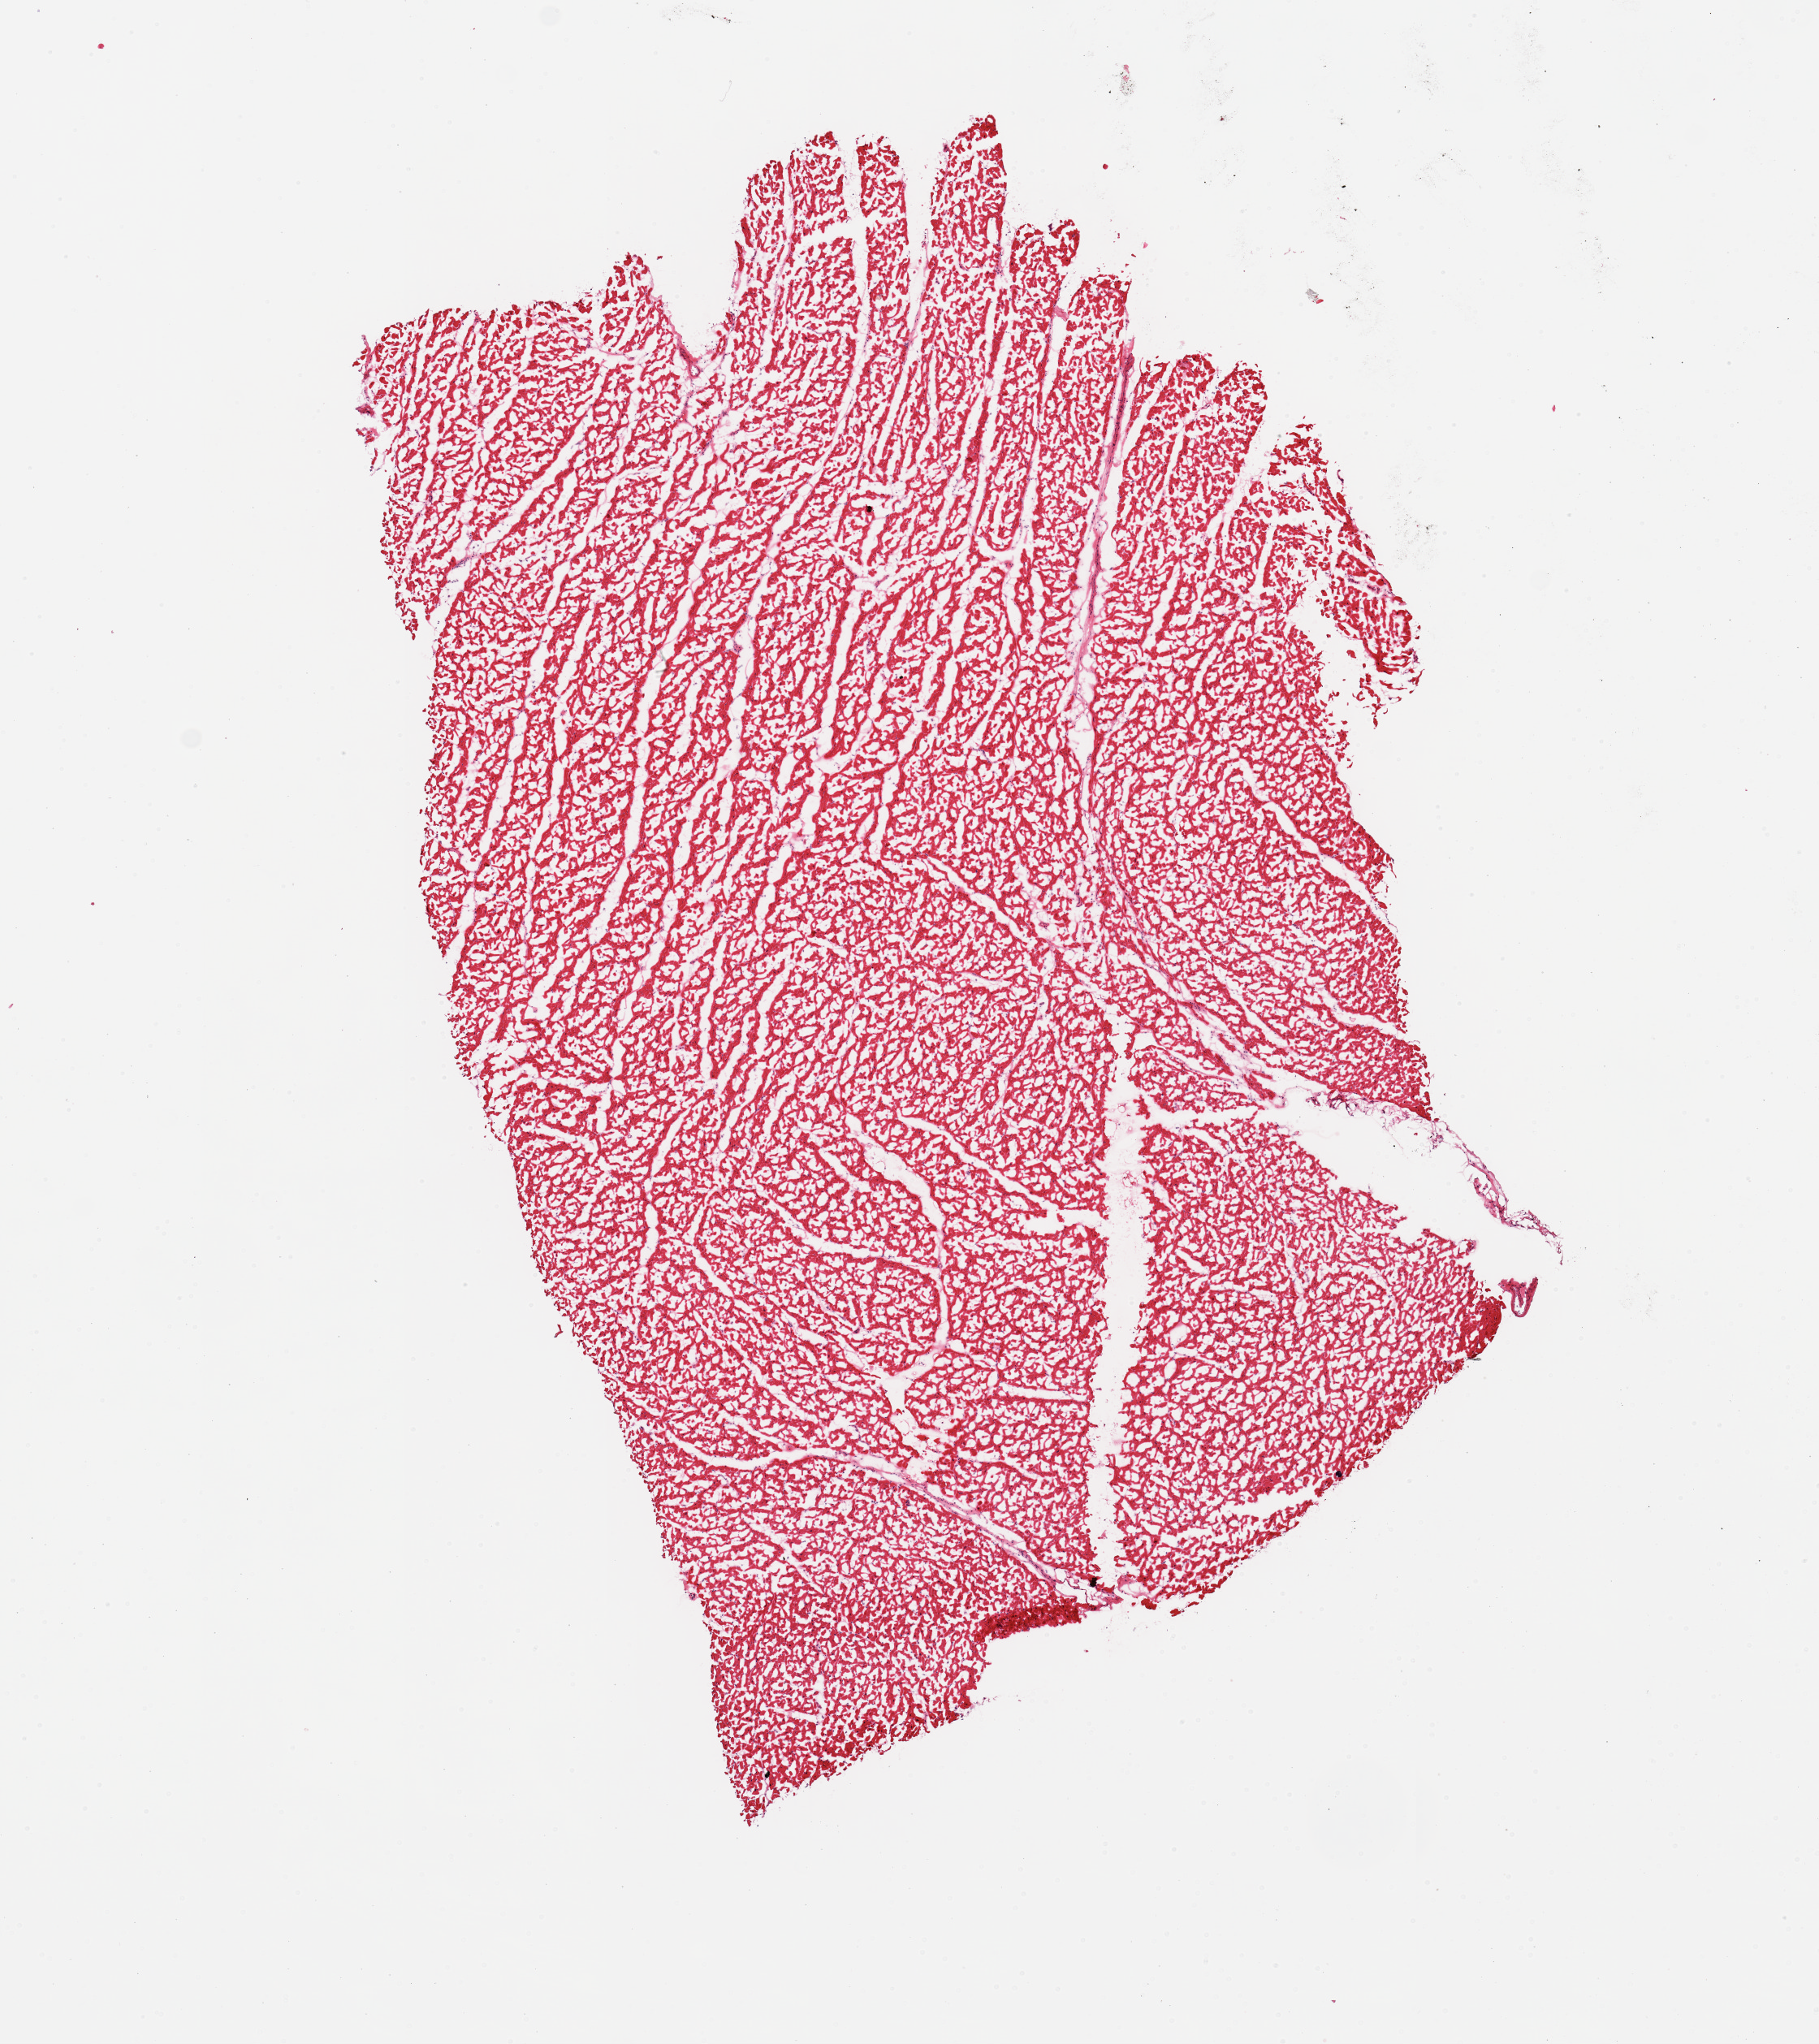
H&E whole-slide image — whole scanned area (about 8.9 x 10.0 mm, acquisition: 20x scan) shown as a low-resolution overview, frozen section (dry ice), section of heart (target tissue), tissue donor sample. Female donor.
• review note (as recorded): 1 piece